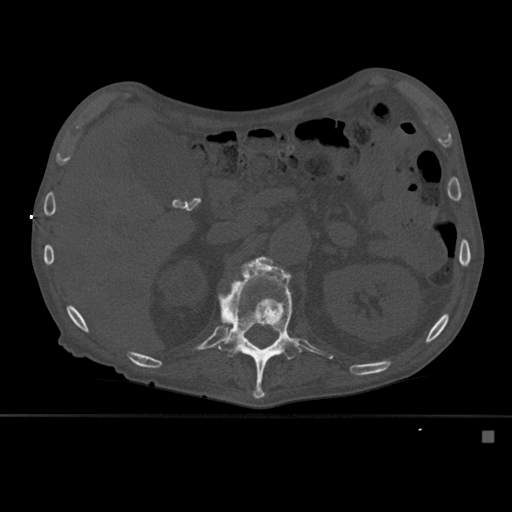
CT including the spine, one axial slice. Slice 257 of 527 in the series (ordered by position). Bone window (W 1800 / L 400 HU). 1.5 mm slice thickness. 512 × 512 image matrix, field of view 373 × 373 mm. Male patient, age 78 years. From the clinical record (not read from this slice): primary cancer: prostate.
Outlined on this slice (semi-automatic segmentation, software-assisted and operator-edited):
- L1 vertebra: bounding box [x1, y1, x2, y2] px = [218, 257, 302, 399]